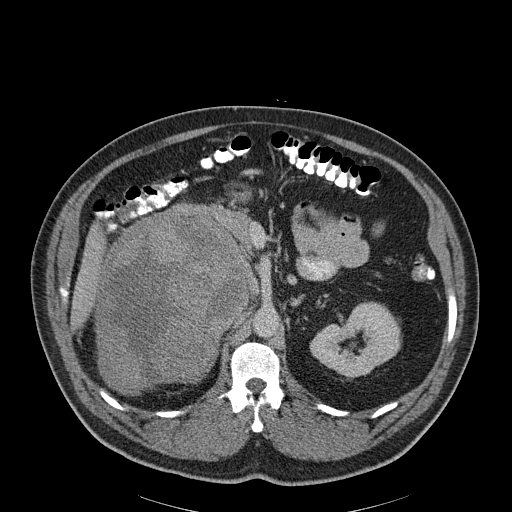
Contrast-enhanced abdominal CT, one axial slice. Slice 125 of 186 in the series (ordered by position). Reconstruction kernel B30f. 120 kVp. Soft-tissue window (W 400 / L 40 HU). 3 mm slice thickness. 512 × 512 image matrix, field of view 464 × 464 mm. Patient: male, 56 years. Case-level facts recorded for this patient, not image findings: diagnosis: adrenocortical carcinoma; tumour side: right adrenal; tumour size at pathology: 18 cm; Ki-67 index: 2 %.
Structures marked on this image (semi-automatic segmentation, software-assisted and operator-edited):
- mass: bounding box [x1, y1, x2, y2] px = [99, 209, 246, 393]